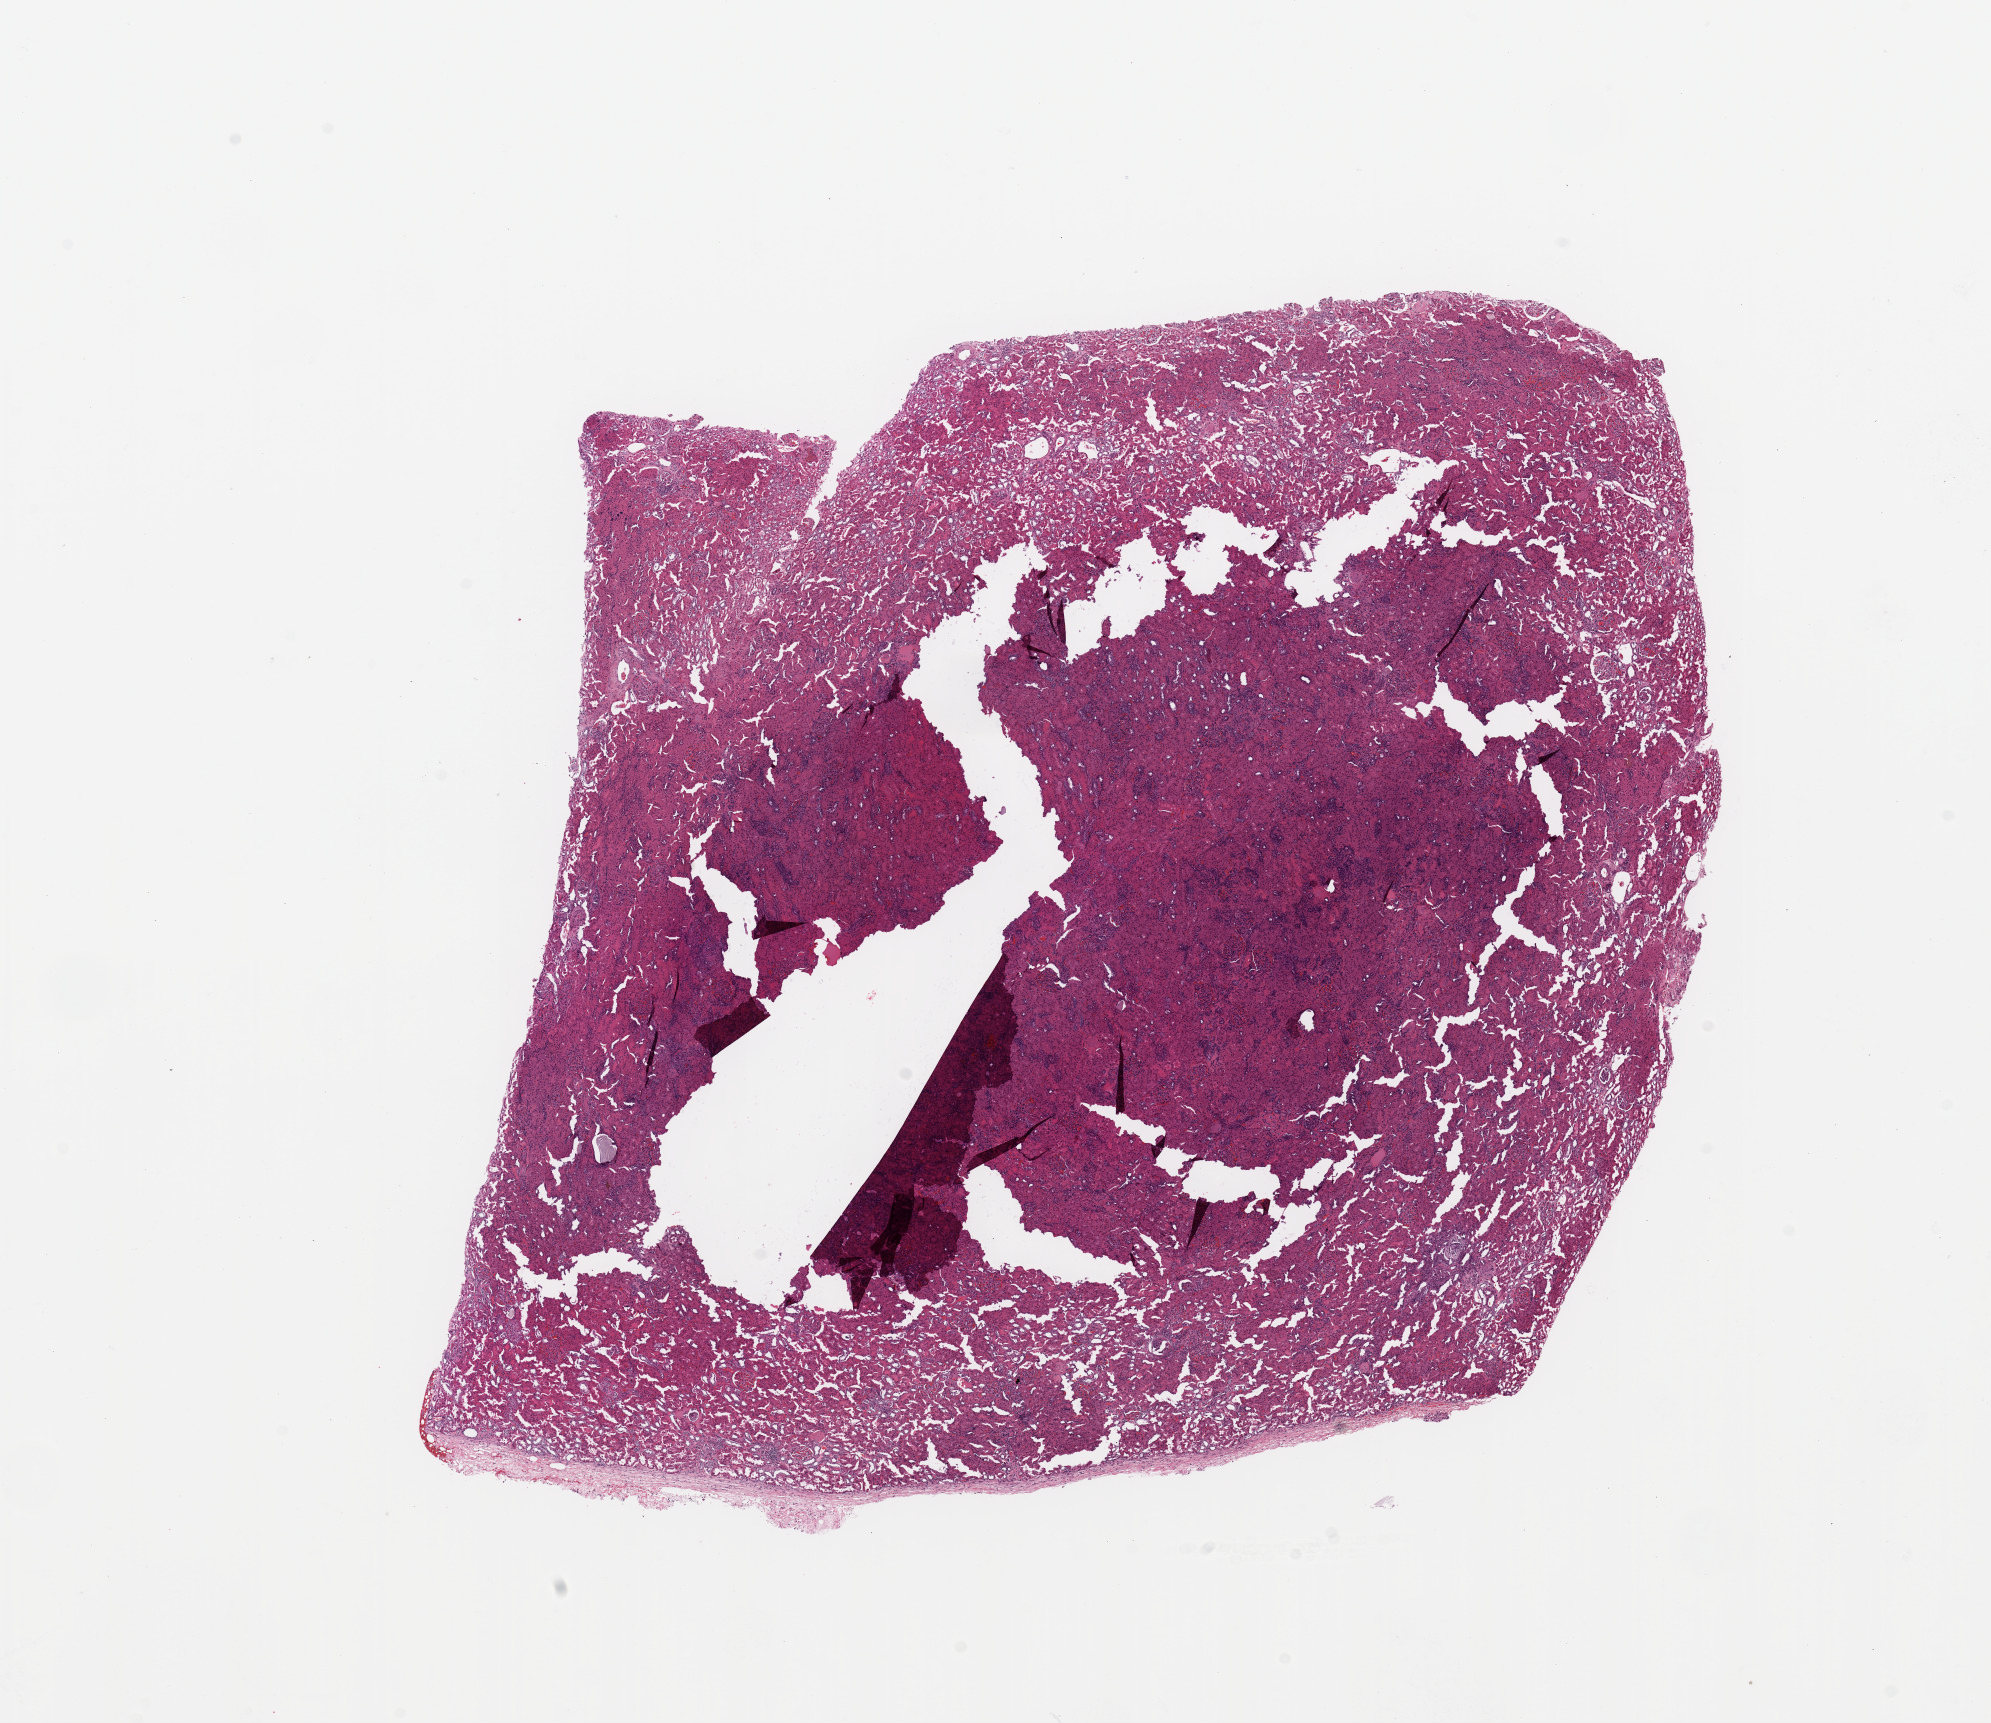
Digitized Hematoxylin and eosin (H&E) stained tissue section (whole slide), a low-resolution overview of the entire scanned area, about 15.8 x 13.6 mm. Normal (non-tumour) tissue sample, kidney. Male, 61 y/o.
This section: normal (non-tumour) tissue from the same patient. Patient diagnosis: Renal cell carcinoma, NOS.